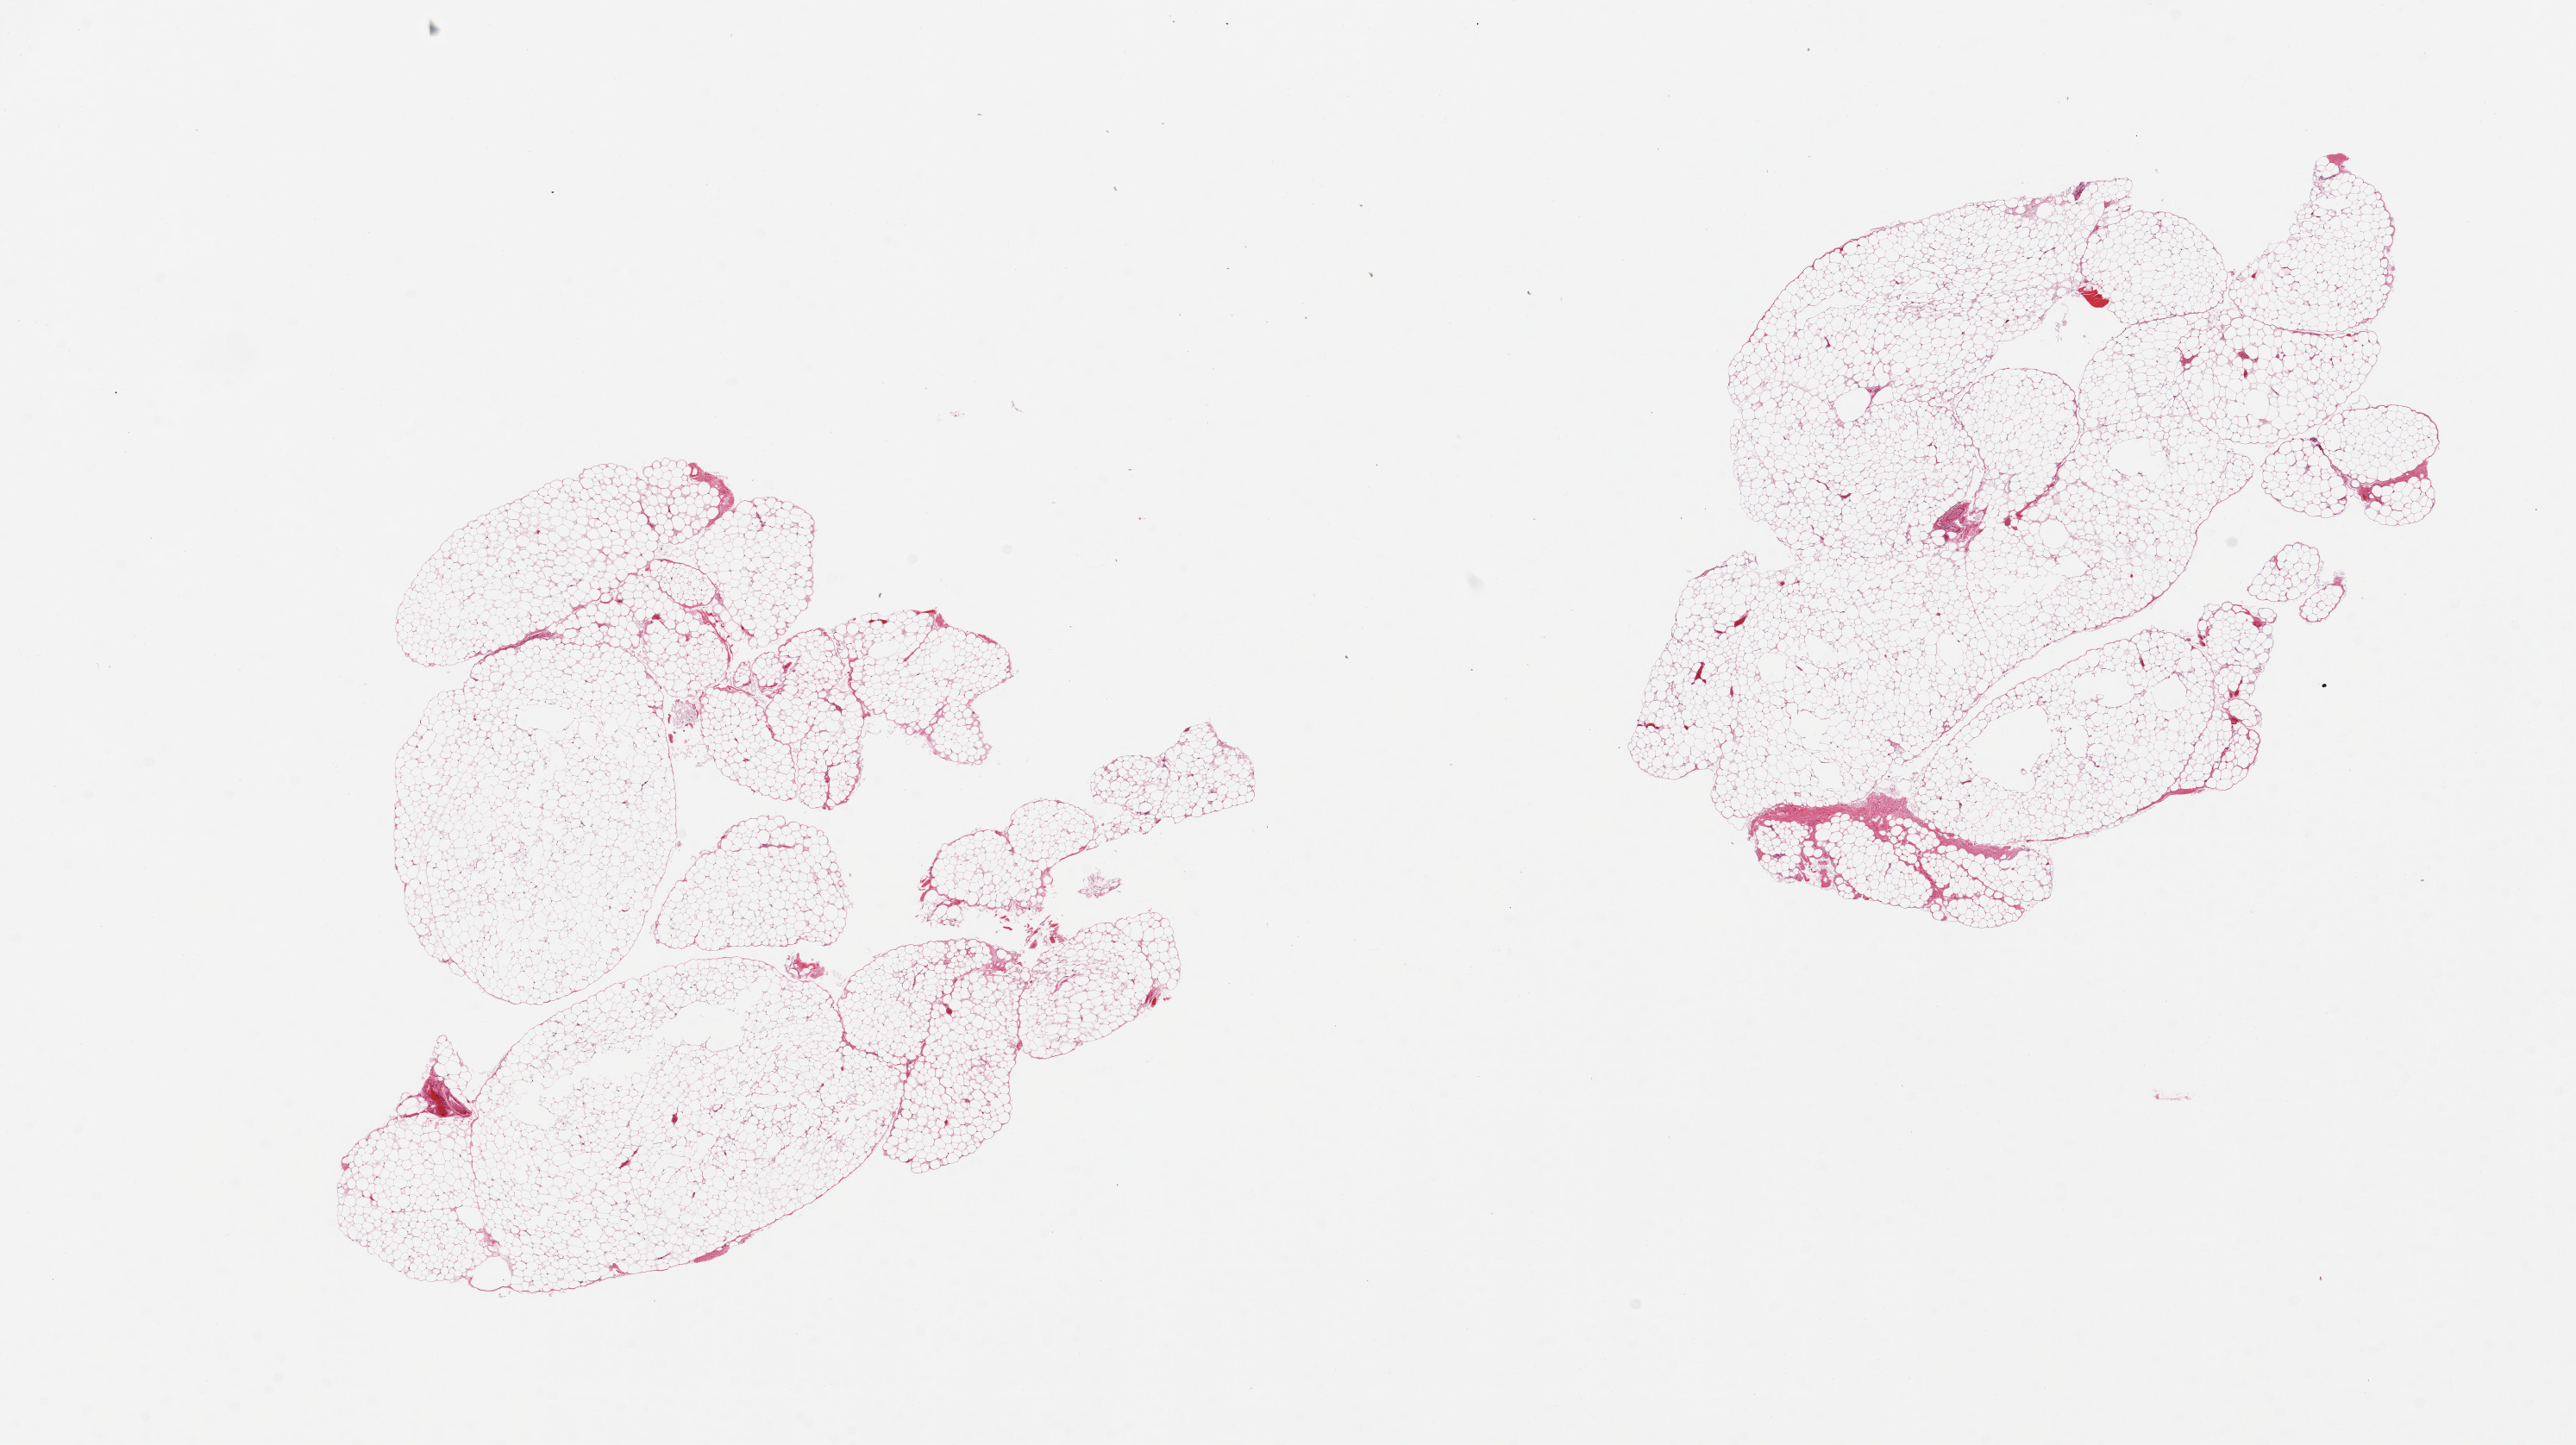
Haematoxylin and eosin whole-slide image, shown as a low-resolution overview of the whole scanned area (about 23.6 x 13.3 mm, acquisition: 20x scan). PAXgene-fixed, paraffin-embedded tissue. Sampled site (target tissue): omentum. Donor tissue sample. Donor: female.
• review note (as recorded): 2 pieces, ~5% fascia/vascular elements